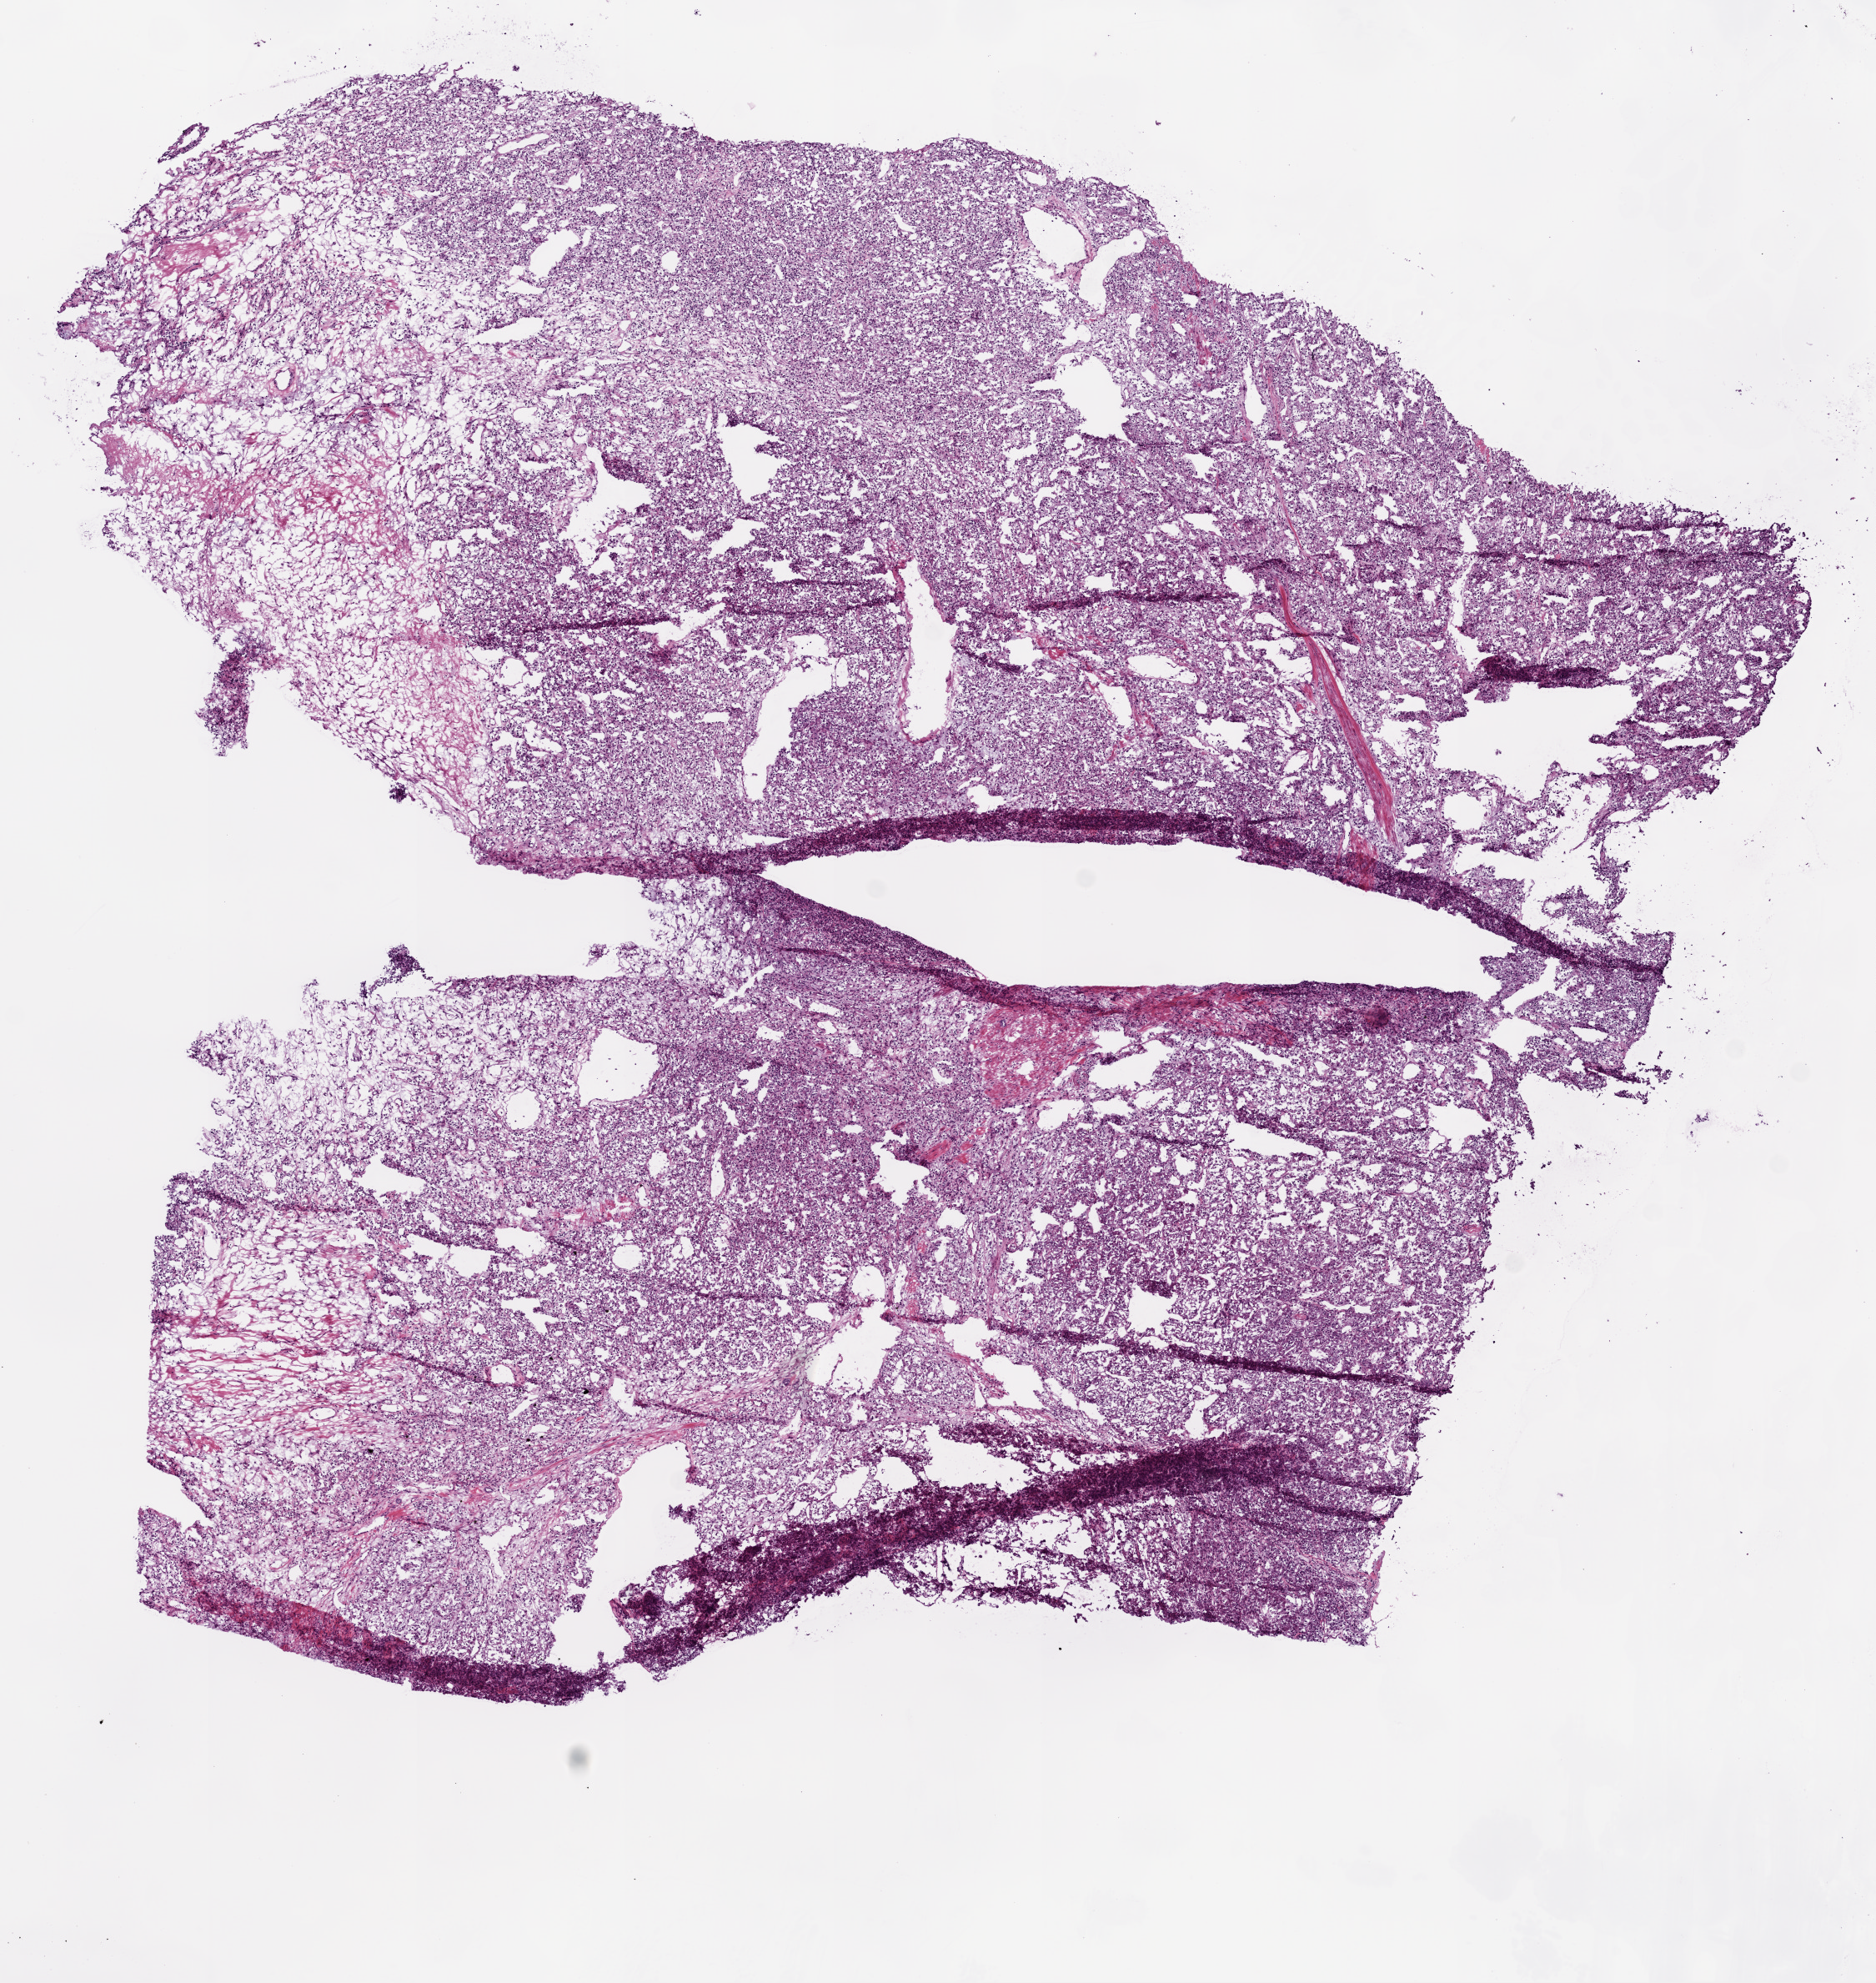
Digitized Hematoxylin and eosin (H&E) stained tissue section (whole slide) — low-resolution overview of the scanned area, about 9.0 x 9.5 mm. Frozen section from the bottom of the tissue portion. Primary tumour sample from the kidney. Patient: male, age at initial diagnosis 69 years. Histologic grade: G4 (undifferentiated). Pathologist review of this section (percent, as recorded): tumour cells 88%, tumour nuclei 85%, normal cells 0%, stromal cells 12%, necrosis 0%.
* pathologic diagnosis: Clear cell adenocarcinoma, NOS
* AJCC pathologic stage: III (6th edition)